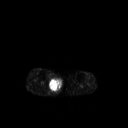
FDG PET of an extremity soft-tissue mass (from a PET/CT study), one axial slice. Position 141 of 267 along the scan axis. 128 × 128 image matrix, field of view 500 × 500 mm. Patient: male, 69 years. Case-level facts recorded for this patient, not image findings: histological type: pleiomorphic liposarcoma; grade: high; site of the primary tumour: right calf.
Structures marked on this image (expert contour drawn on MRI and transferred to this co-registered scan by the dataset authors):
- gross tumour volume including surrounding oedema: bounding box <49,76,62,92> (left, top, right, bottom; pixels)
- gross tumour volume (mass): <50,78,62,91>